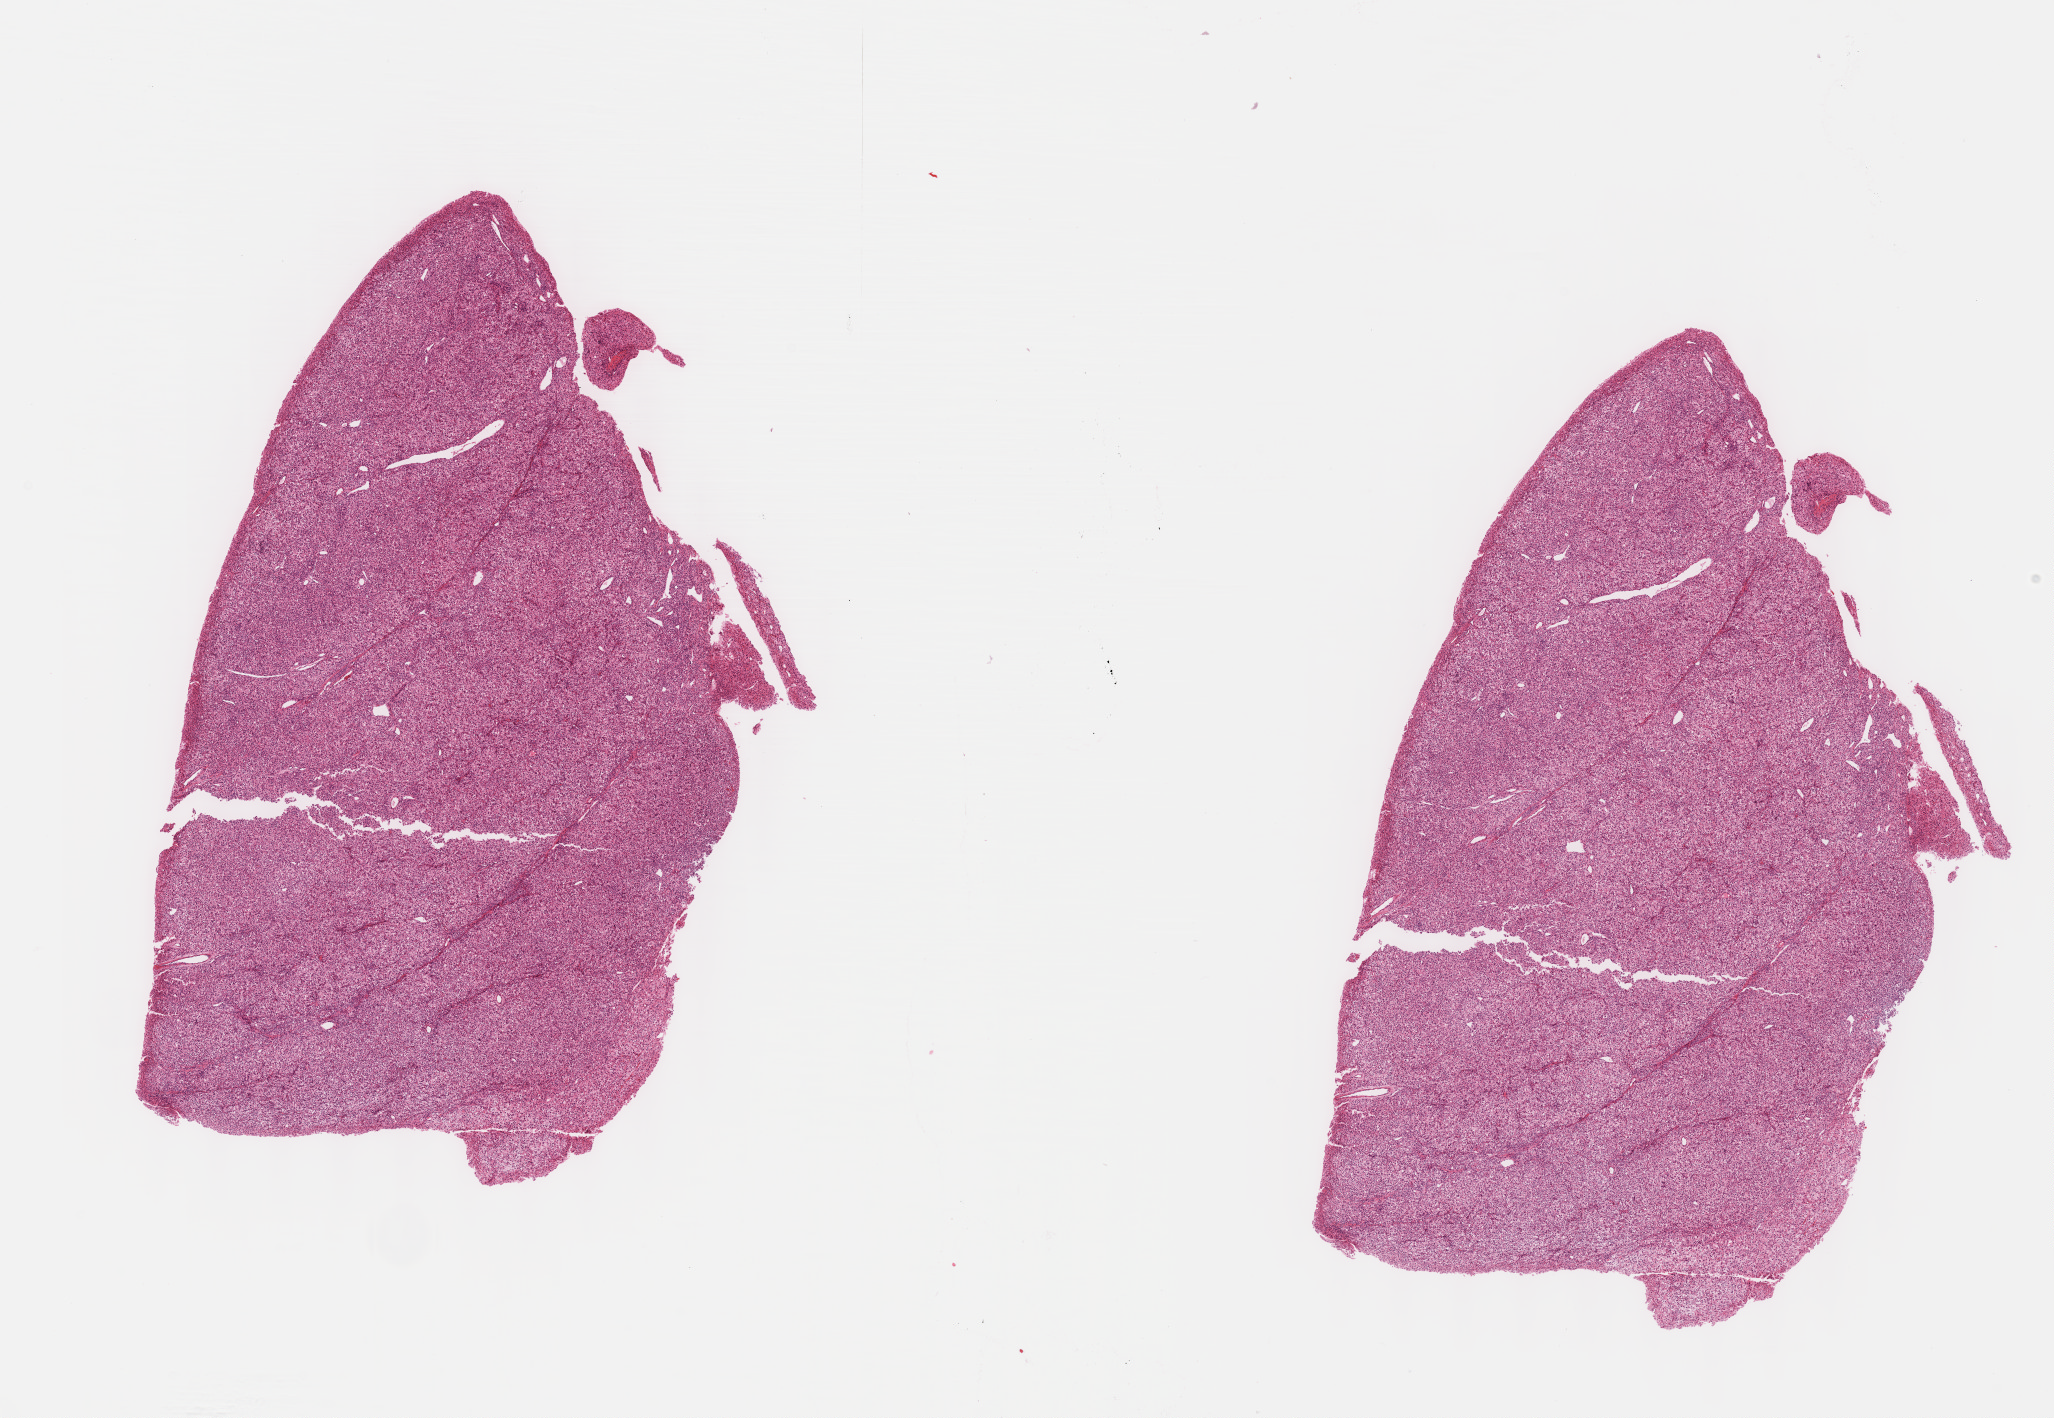
Whole-slide histology image, H&E-stained — low-resolution overview of the scanned area, about 16.6 x 11.5 mm (slide scanned at 40x). Formalin-fixed paraffin-embedded (FFPE) diagnostic section. Sample: primary tumour, liver. Patient: female, age at initial diagnosis 55 years. Histologic grade: G2 (moderately differentiated).
AJCC pathologic stage: I (7th edition). Histologic diagnosis: Hepatocellular carcinoma, NOS.